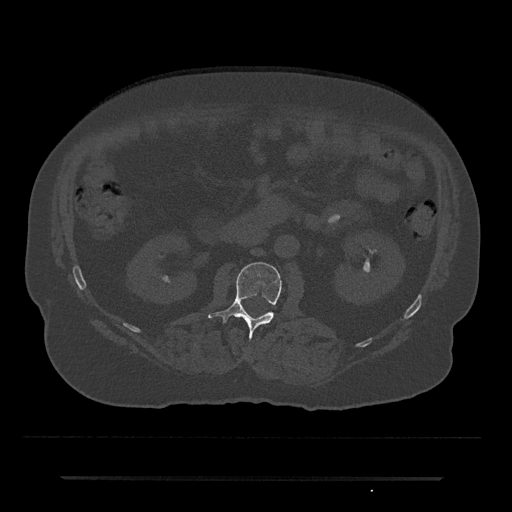
CT including the spine, one axial slice; slice 11 of 797 in the series (ordered by position); reconstruction kernel Br40s/3; bone window (W 1800 / L 400 HU); 512 × 512 image matrix, field of view 437 × 437 mm. Patient: male, 69 years. Case-level facts recorded for this patient, not image findings: primary cancer: prostate.
Structures marked on this image (semi-automatic segmentation, software-assisted and operator-edited):
- L2 vertebra: bounding box <208,262,282,339> (left, top, right, bottom; pixels)